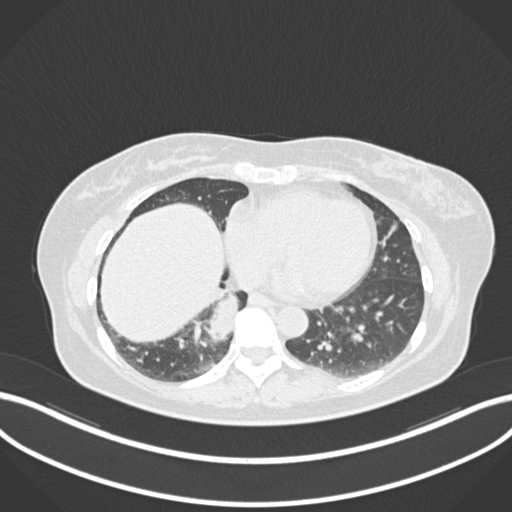
Chest CT, one axial slice; position 548 of 677 along the scan axis; reconstruction kernel B30f; 120 kVp; lung window (W 1500 / L -600 HU); 1 mm slice thickness; 512 × 512 image matrix. Patient: female, 54 years. From the clinical record (not read from this slice): clinical TNM (as recorded): T4 N0 M0.
Annotated regions visible in this slice (bounding box drawn by a radiologist):
- lung tumour (recorded histology: adenocarcinoma): bounding box <207,288,241,344> (left, top, right, bottom; pixels)